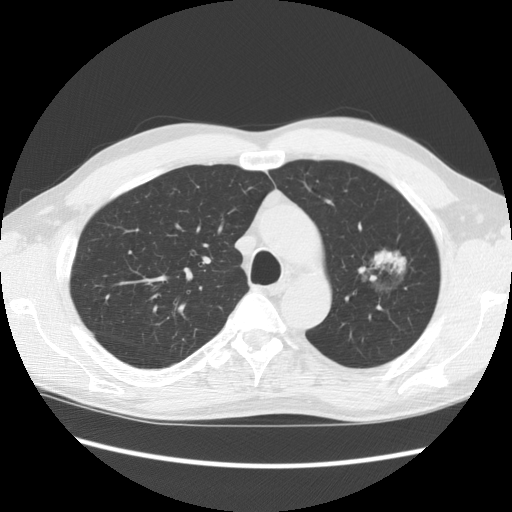
Chest CT (low-dose screening protocol), one axial image; second annual screen; lung window (W 1500 / L -600 HU). Male participant, aged 61 years at enrolment. Former smoker at enrolment.
Lesion marked by an expert reader, bounding box [x1, y1, x2, y2] px = [347, 225, 423, 299]. Reader record for this screening exam (exam-level; its link to the box is not recorded): non-calcified nodule or mass ≥4 mm, left upper lobe, 34 × 32 mm, poorly defined margins, mixed attenuation, pre-existing on the prior screen: yes; interval growth: no. Official screen result: positive, no significant change: stable abnormalities potentially related to lung cancer, unchanged since the prior screening exam. Later outcome: lung cancer diagnosed 704 days after this screen — bronchiolo-alveolar adenocarcinoma, NOS, left upper lobe, well differentiated (G1), stage IB (AJCC 6th edition), 44 mm at pathology.